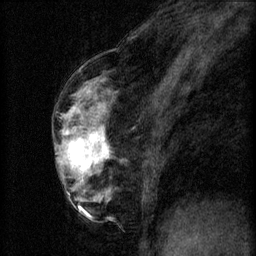
Breast MRI (dynamic contrast-enhanced), one sagittal slice. Position 30 of 60 along the scan axis. 3 images stored at this slice position (order not interpretable as contrast timing). 1.5 T. TE 4.2 ms, TR 8.2 ms. 2 mm slice thickness. 256 × 256 image matrix, field of view 180 × 180 mm. Female patient, age 56 years.
Structures marked on this image (semi-automatically segmented with operator editing):
- analysis volume of interest (the breast-tissue region the enhancement analysis was run in; not a lesion): bounding box (x1, y1, x2, y2) in pixels: (60, 124, 110, 179)
- tumour enhancement mask (voxels above the 70 % enhancement threshold inside the analysis volume of interest): (63, 128, 108, 171)